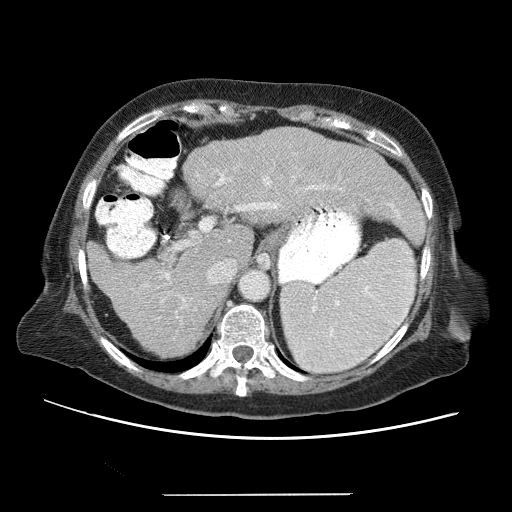
Contrast-enhanced abdominal CT (liver protocol), one axial slice; slice 41 of 65 in the series (ordered by position); 120 kVp; soft-tissue window (W 400 / L 40 HU); 2.5 mm slice thickness; 512 × 512 image matrix. Case-level facts recorded for this patient, not image findings: diagnosis: hepatocellular carcinoma (patient treated with transarterial chemoembolisation; whether this scan precedes or follows treatment is not stated here); TNM stage (as recorded): Stage-IIIB; Child-Pugh class: A; tumour differentiation: moderately differentiated; tumour nodularity: uninodular.
Outlined on this slice (semi-automatic segmentation, software-assisted and operator-edited):
- liver parenchyma outside the tumour (the mass and vessels are separate outlines, so this box may not span the whole liver): box from (x=86, y=128) to (x=420, y=354) px
- liver vessels: (x=101, y=151)–(x=407, y=339)